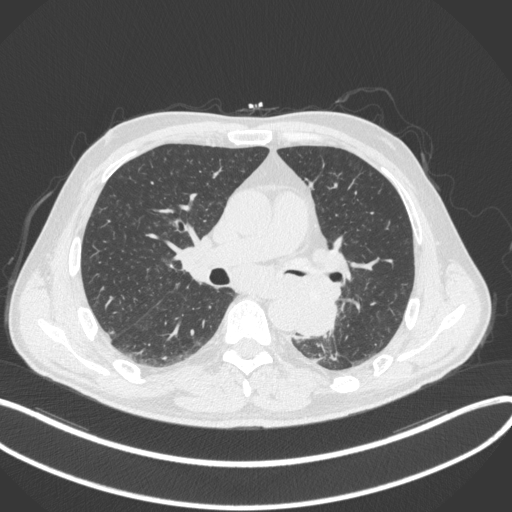
Chest CT, one axial slice; position 194 of 328 along the scan axis; lung window (W 1500 / L -600 HU); 1 mm slice thickness; 512 × 512 image matrix. Male patient, age 59 years. Case-level facts recorded for this patient, not image findings: clinical TNM (as recorded): T2a N2 M0.
Annotated regions visible in this slice (rectangle marked by the reading radiologist):
- lung tumour (recorded histology: squamous cell carcinoma): box from (x=295, y=287) to (x=339, y=341) px